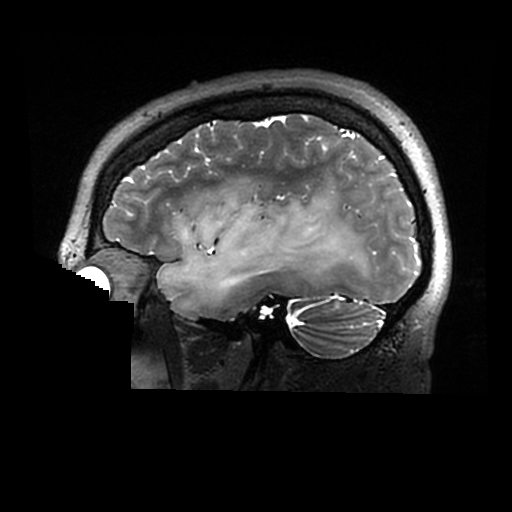
Brain MRI from a brain-tumour surgery series, one sagittal slice; position 218 of 320 along the scan axis; 0.6 mm slice thickness; 512 × 512 image matrix. Case-level facts recorded for this patient, not image findings: histopathology: Astrocytoma; WHO grade: 2; IDH mutation: yes.
Outlined on this slice (outlined manually by an expert reader):
- tumour: bounding box [x1, y1, x2, y2] px = [157, 188, 378, 310]